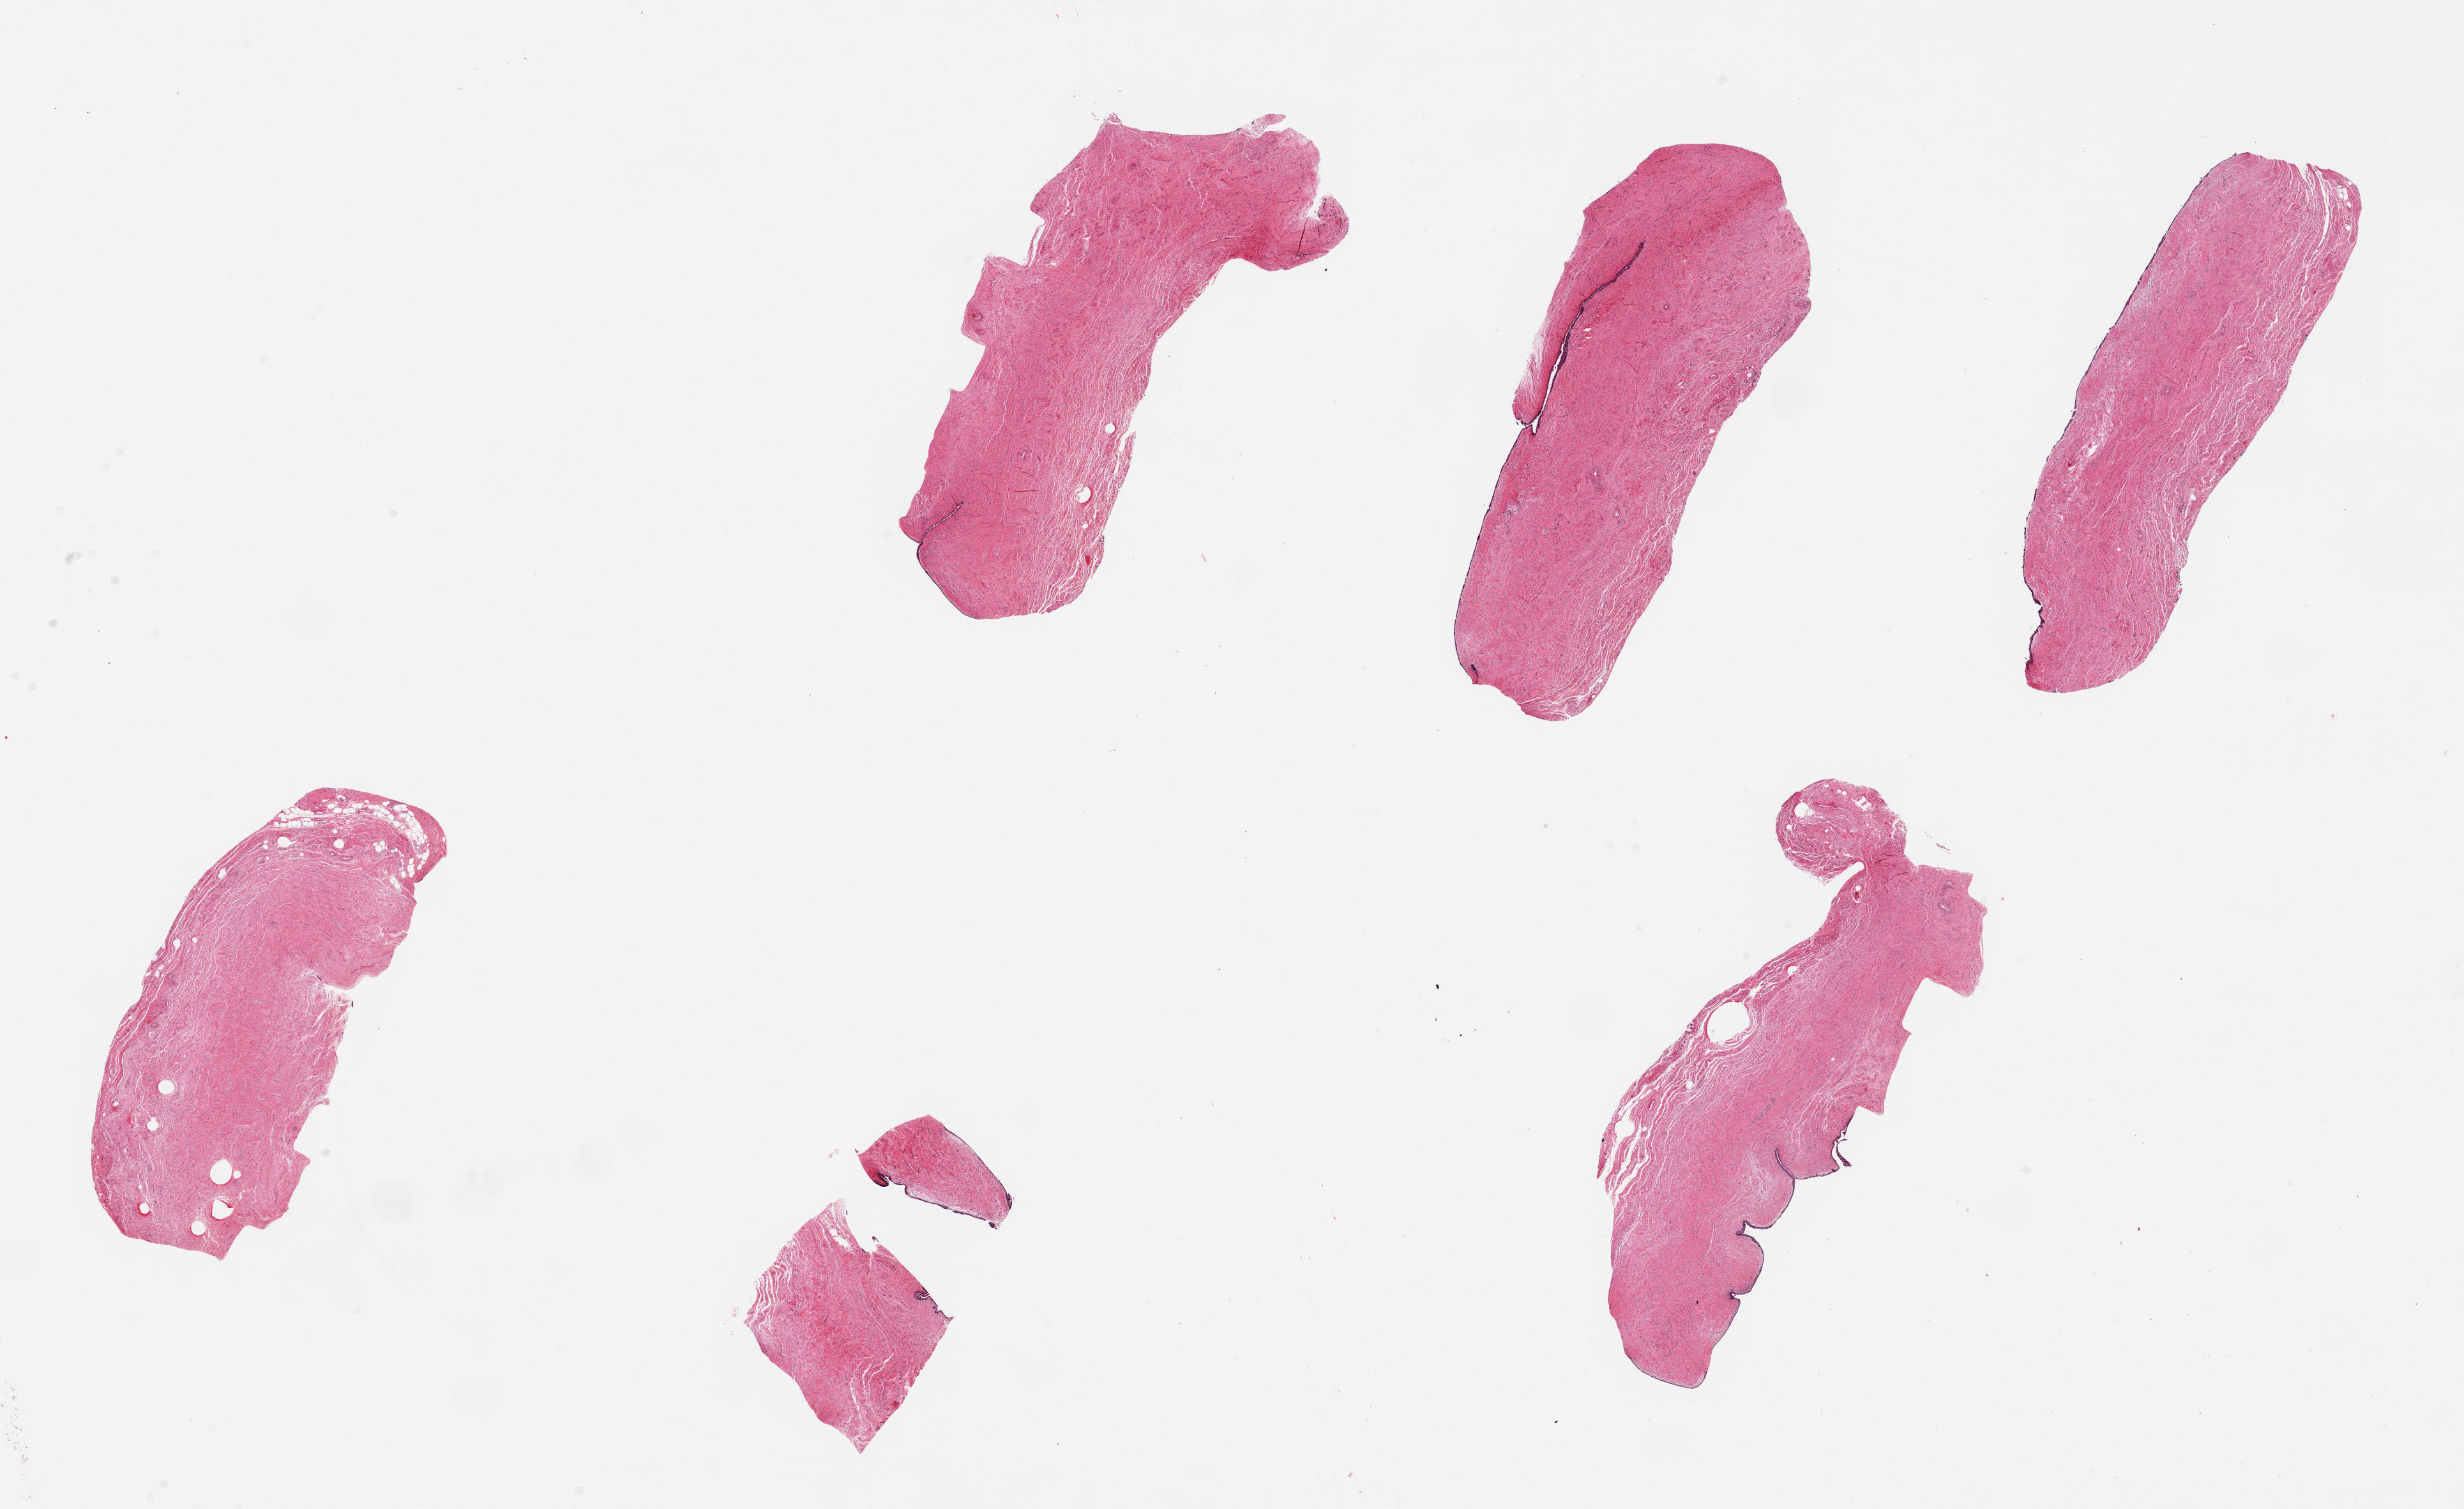
Digitized hematoxylin and eosin (H&E)-stained section, brightfield — a low-resolution overview of the entire scanned area, about 30.5 x 18.7 mm (slide scanned at 20x). PAXgene-fixed, paraffin-embedded tissue. Target tissue: vagina. Tissue donor sample. Donor sex: female.
• pathologist's review note for this sample: 6 pieces. up to 8x3mm; atrophic epithelium =2; wall = 1